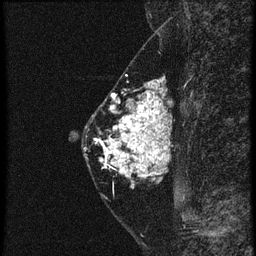
Breast MRI (dynamic contrast-enhanced), one sagittal slice. 4 images stored at this slice position (order not interpretable as contrast timing). 1.5 T. TE 4.2 ms, TR 20.4 ms. 1.5 mm slice thickness. 256 × 256 image matrix, field of view 180 × 180 mm. Patient: female, 46 years. Case-level facts recorded for this patient, not image findings: setting: breast cancer imaged before/during neoadjuvant chemotherapy; receptor status: triple-negative.
Annotated regions visible in this slice (semi-automatically segmented with operator editing):
- analysis volume of interest (the breast-tissue region the enhancement analysis was run in; not a lesion): bounding box [x1, y1, x2, y2] px = [88, 82, 169, 185]
- tumour enhancement mask (voxels above the 90 % enhancement threshold inside the analysis volume of interest): [96, 84, 169, 179]